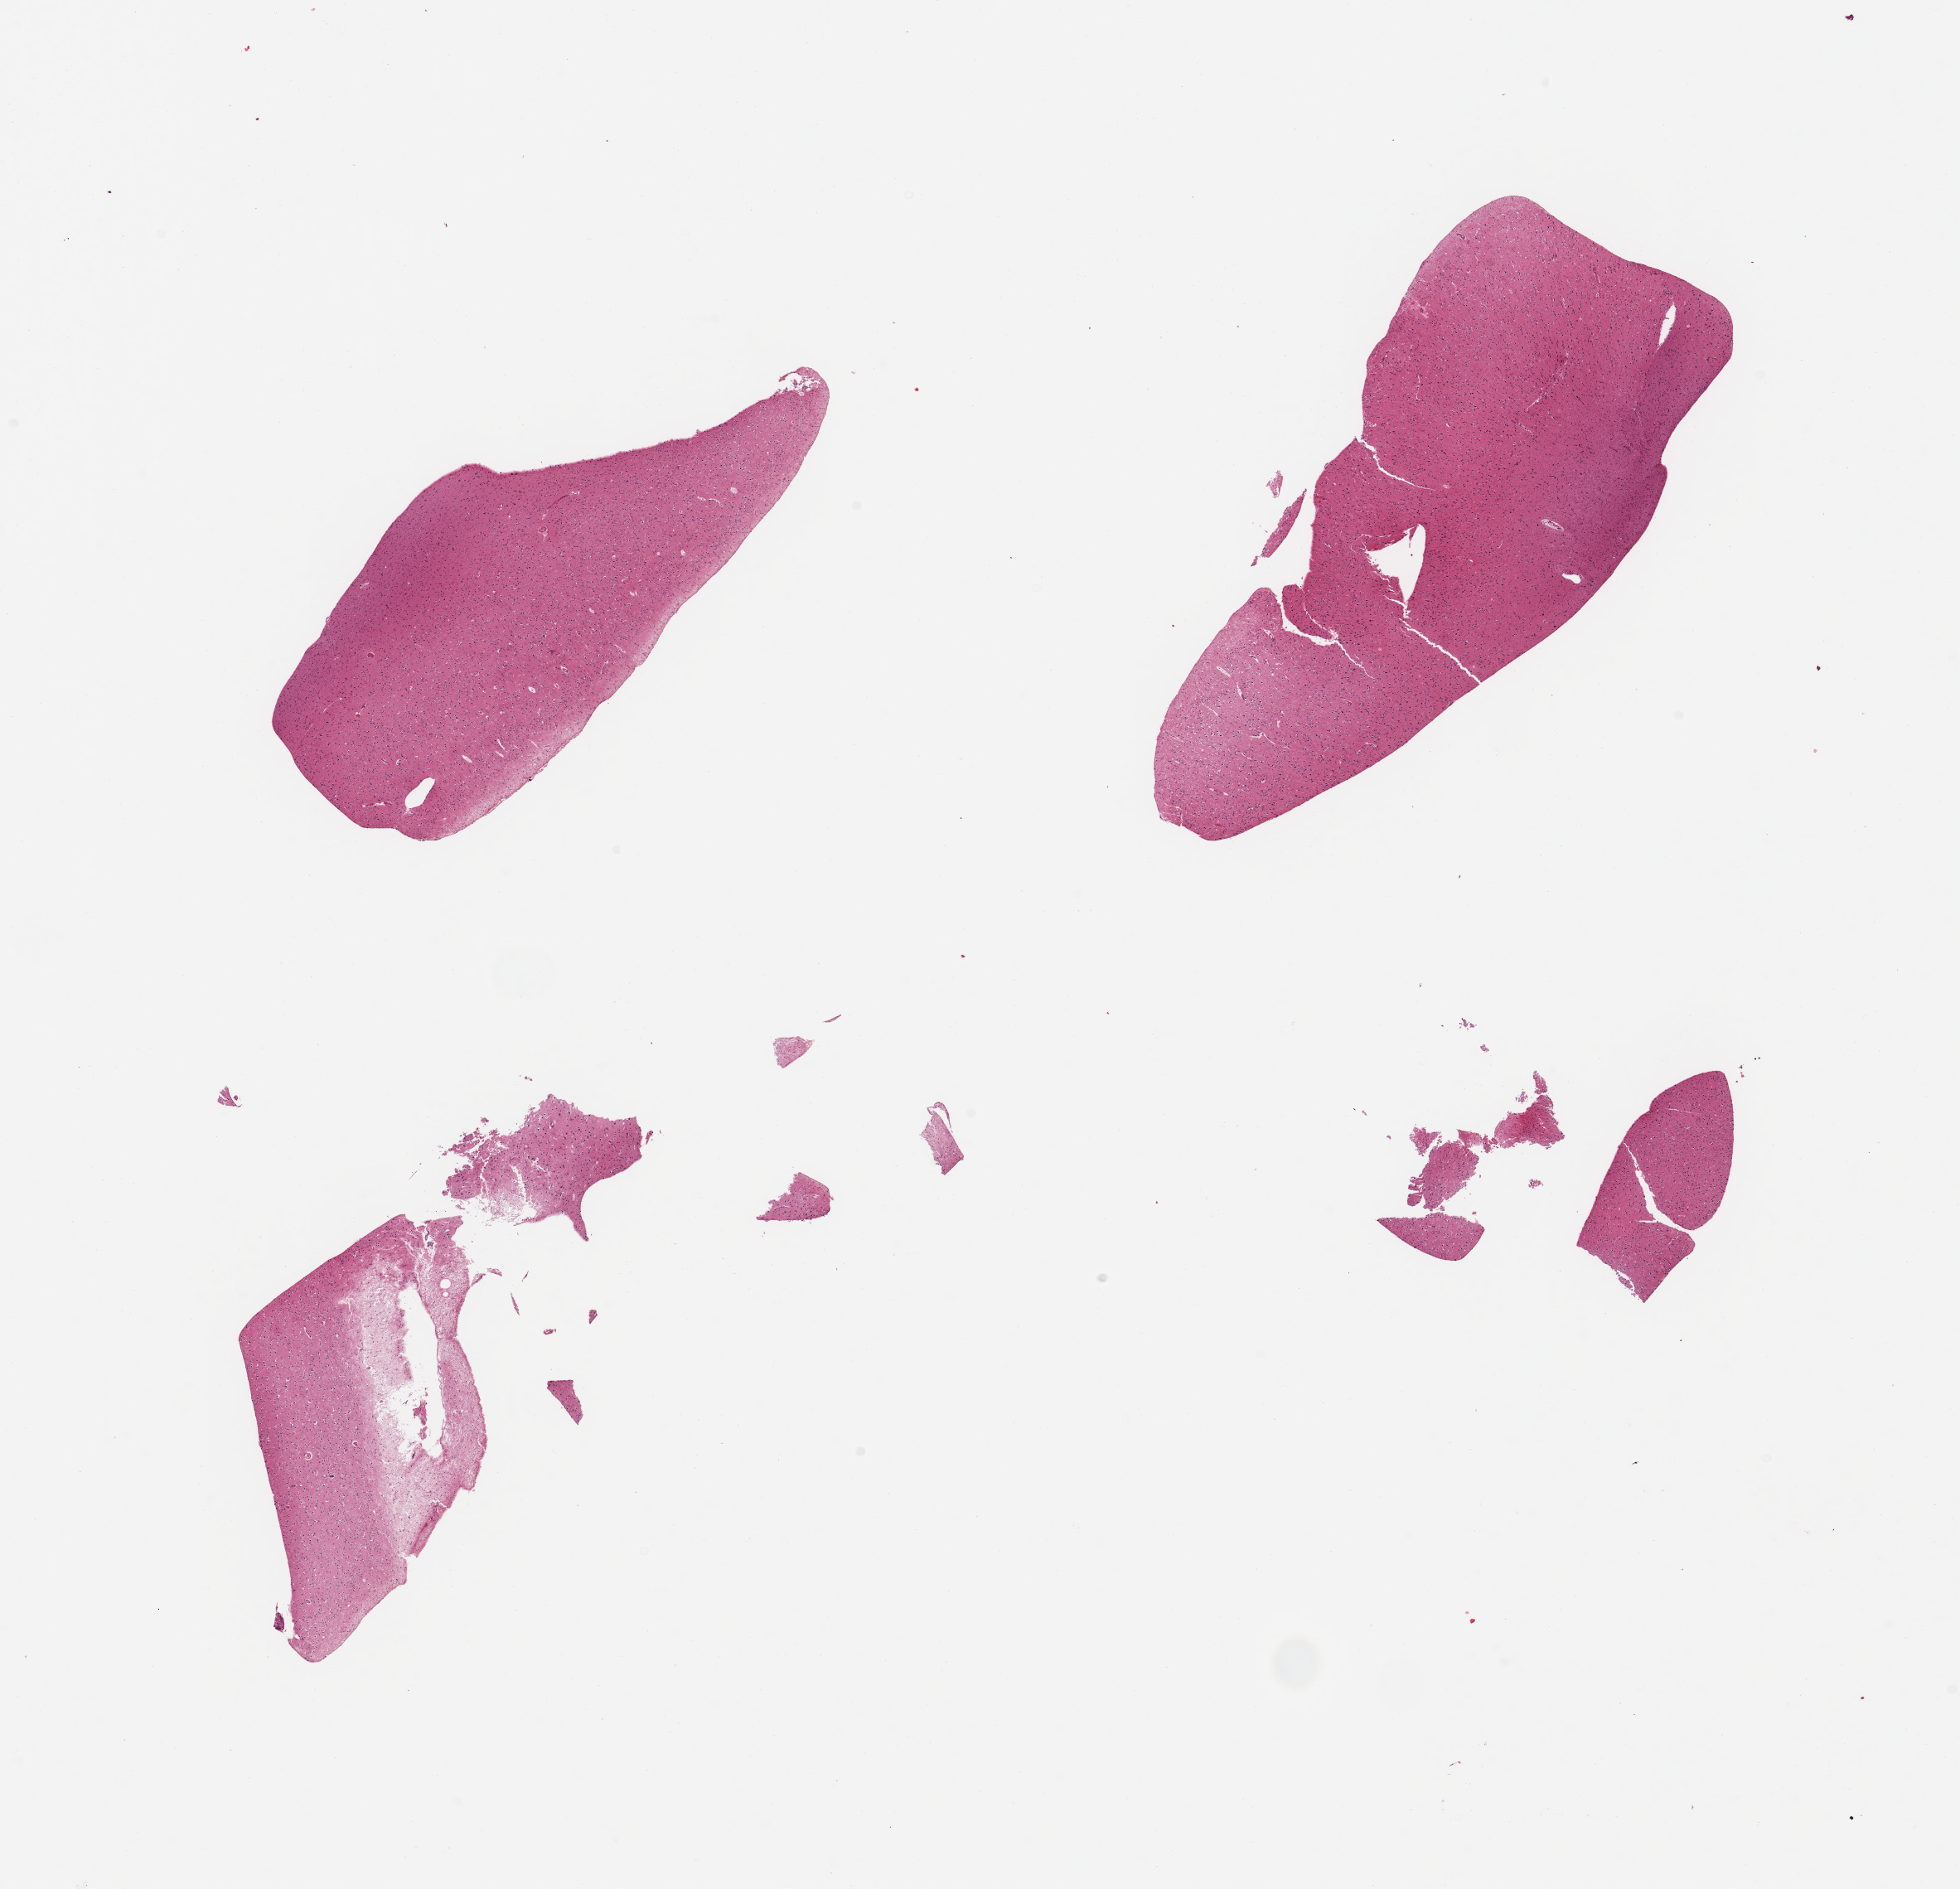
Whole-slide image, haematoxylin and eosin stain, brightfield, whole scanned area (about 18.7 x 18.0 mm, slide scanned at 20x) shown as a low-resolution overview, PAXgene-fixed paraffin-embedded (PFPE) section, sampled site (target tissue): cerebral cortex, donor tissue sample. Donor sex: female.
Review note (as recorded): 4 pieces; 2 pieces are small & fragmented.